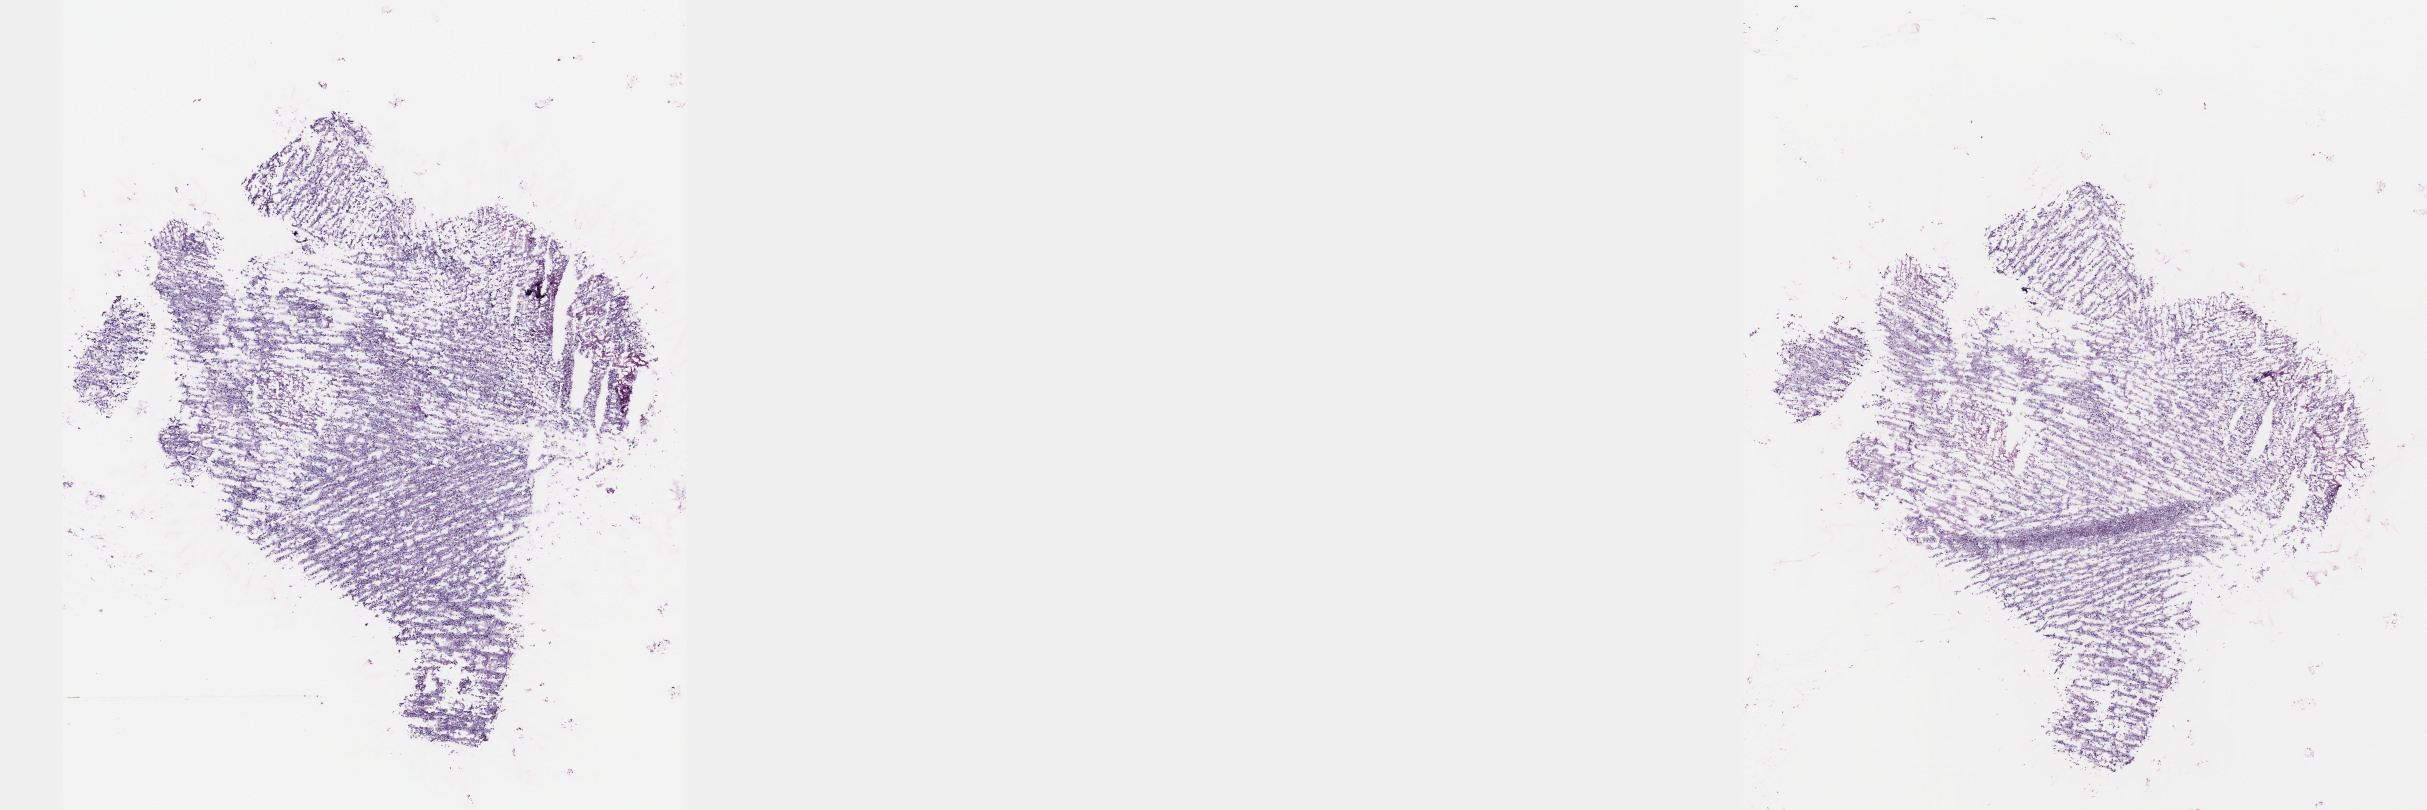
Digitized Hematoxylin and eosin (H&E) stained tissue section (whole slide), shown as a low-resolution overview of the whole scanned area (about 19.6 x 6.5 mm), frozen section from the top of the tissue portion, sample: primary tumour, brain. Male patient; age at initial diagnosis 30 years. Histologic grade: G2 (moderately differentiated). Pathologist review of this section (percent, as recorded): tumour cells 70%, tumour nuclei 90%, normal cells 5%, stromal cells 25%, necrosis 0%. Infiltration values recorded for this section: lymphocyte infiltration 0%, monocyte infiltration 0%, neutrophil infiltration 0%.
- histologic diagnosis: Mixed glioma (cerebrum)
- laterality: left